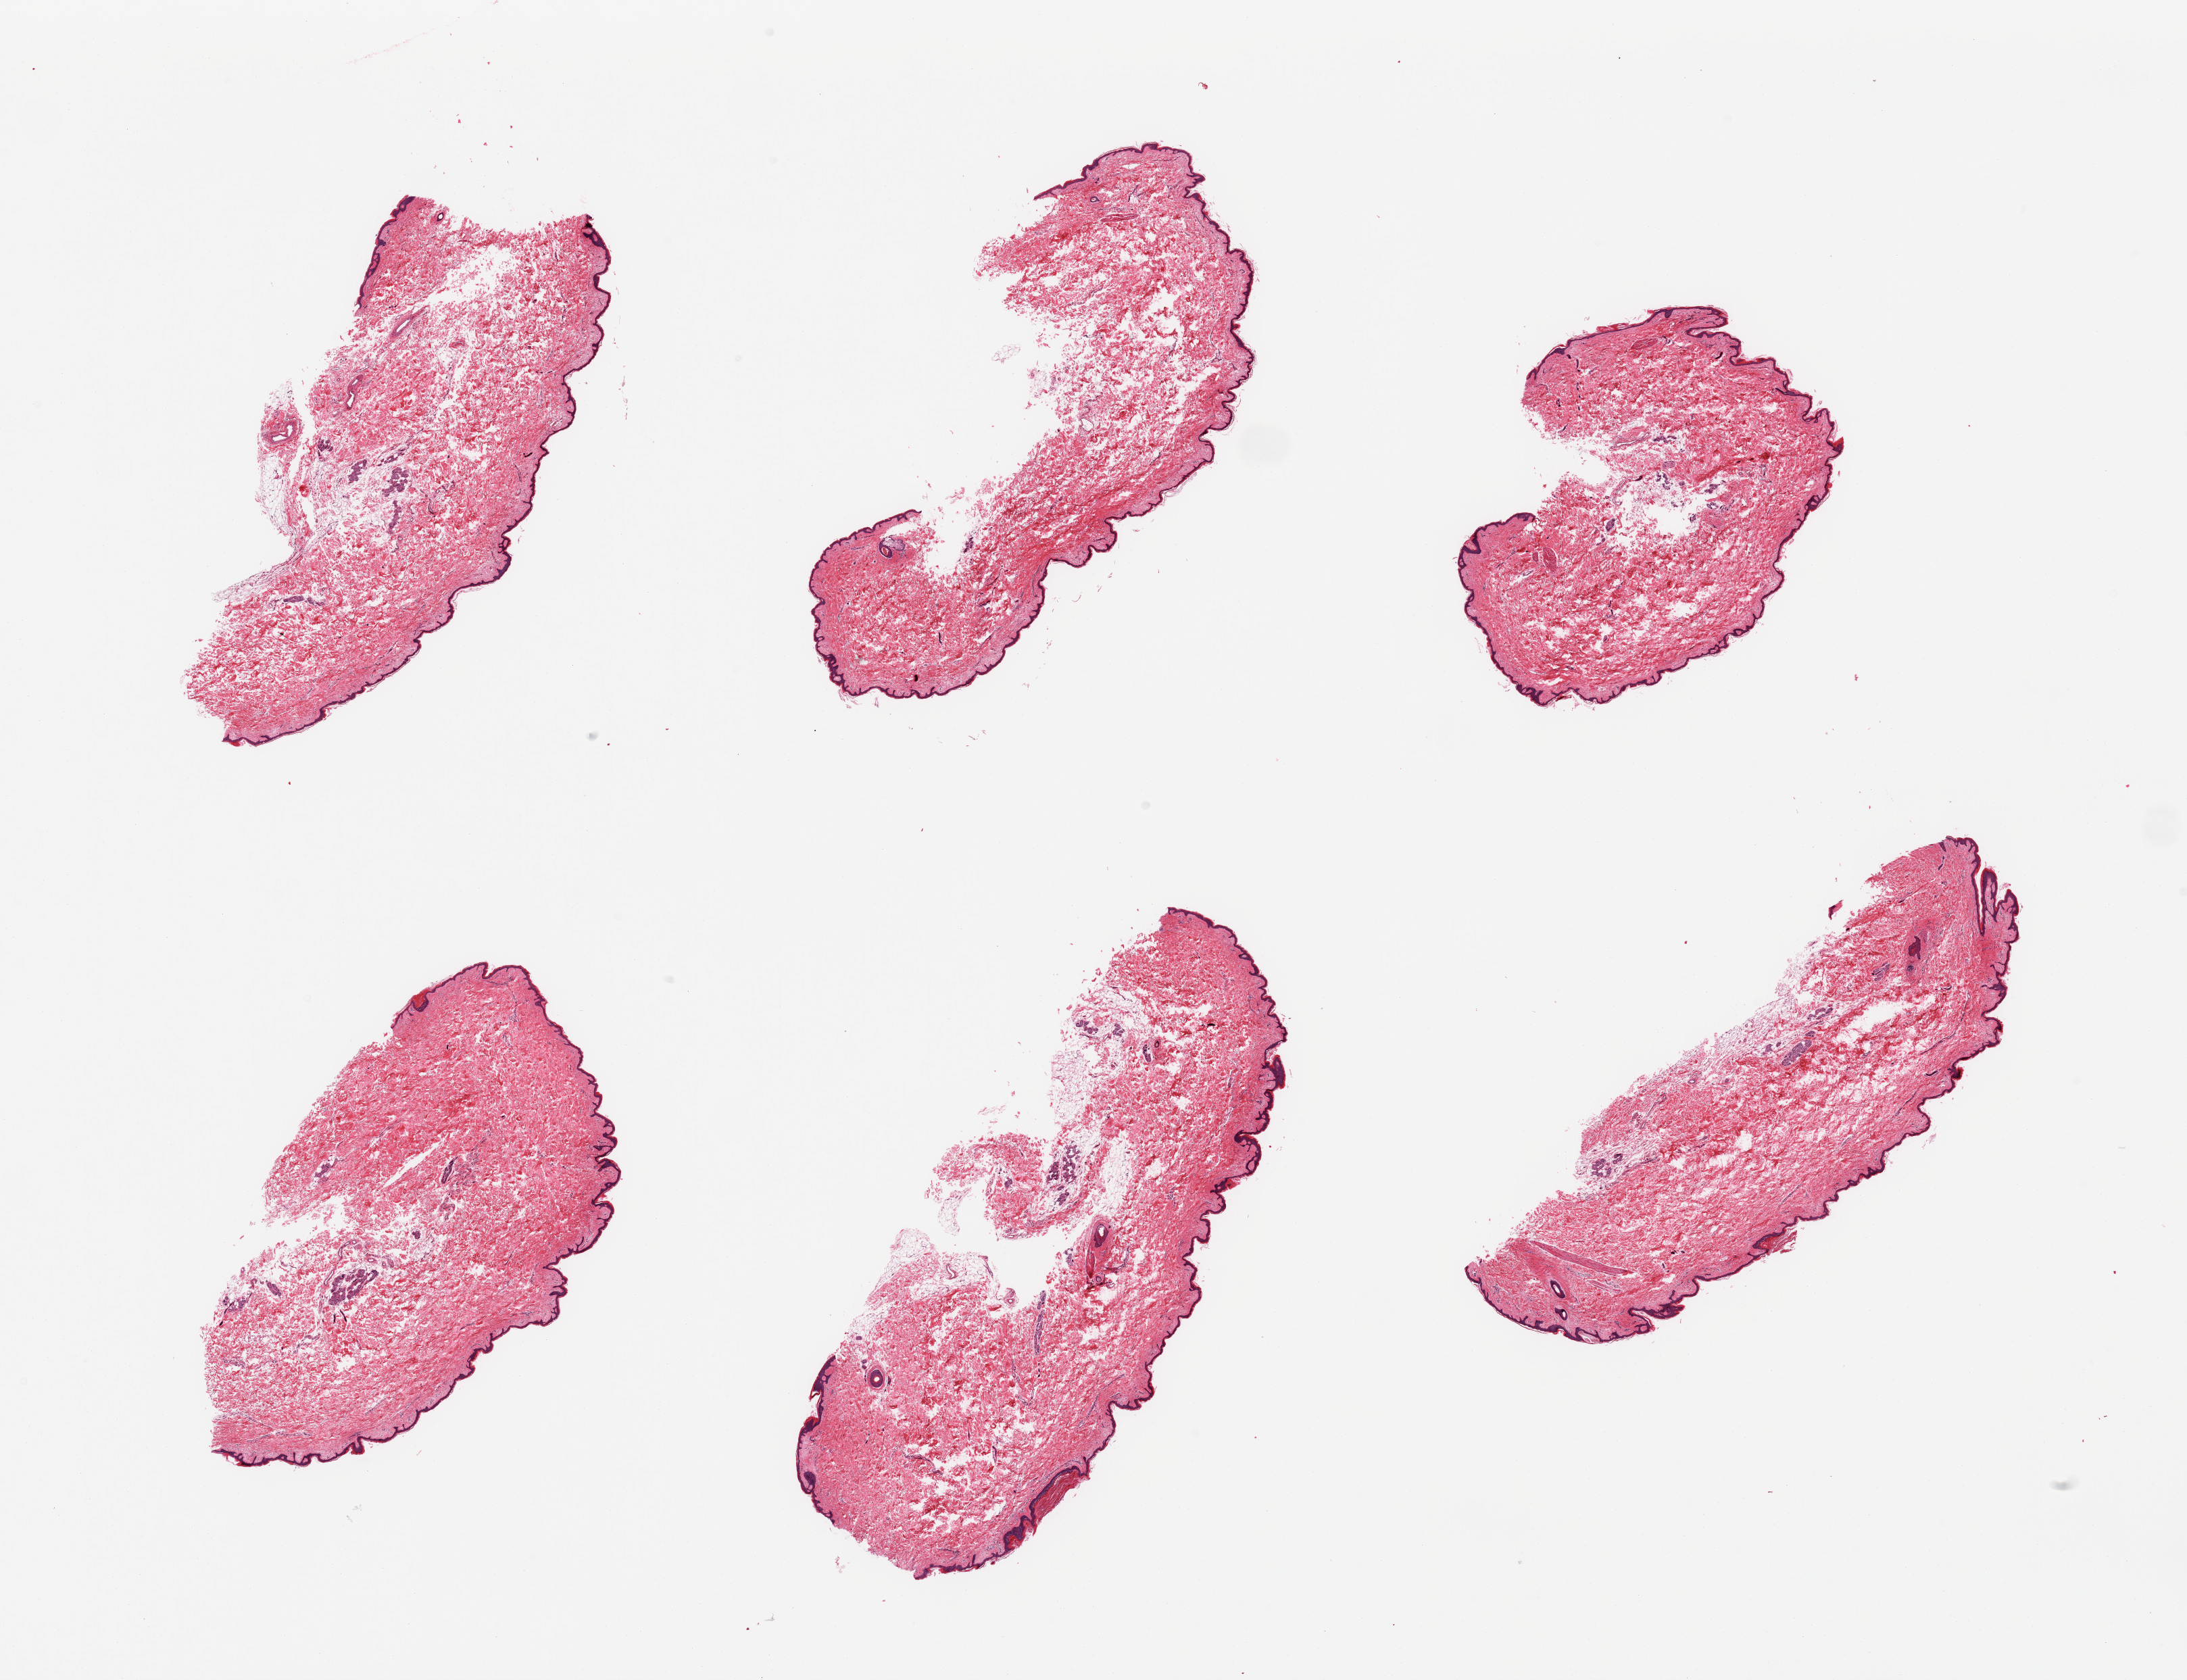
Digitized hematoxylin and eosin (H&E)-stained section, brightfield — whole scanned area (about 25.6 x 19.7 mm) shown as a low-resolution overview; PAXgene-fixed paraffin-embedded (PFPE) section; target tissue: skin of suprapubic region; tissue donor sample. Female donor.
Pathologist's review note for this sample: 6 pieces, moderate dermal fat; Squamous epithelium is ~25 microns.